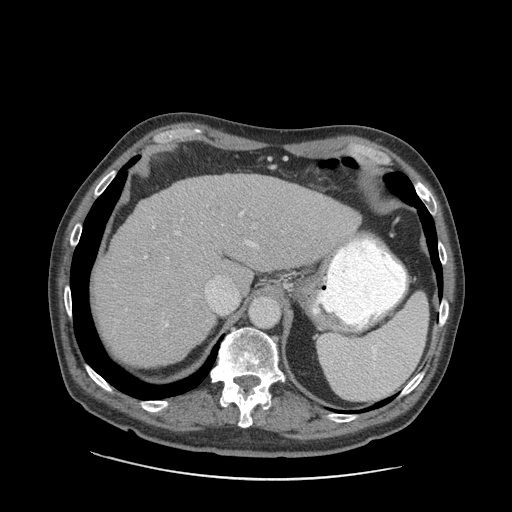
Contrast-enhanced abdominal CT (liver protocol), one axial slice. Slice 66 of 89 in the series (ordered by position). Reconstruction kernel STANDARD. 140 kVp. Soft-tissue window (W 400 / L 40 HU). 2.5 mm slice thickness. 512 × 512 image matrix. Case-level facts recorded for this patient, not image findings: diagnosis: hepatocellular carcinoma (patient treated with transarterial chemoembolisation; whether this scan precedes or follows treatment is not stated here); TNM stage (as recorded): Stage-I; Child-Pugh class: A; tumour nodularity: uninodular; tumour size: 4.6 cm.
Outlined on this slice (semi-automatically segmented with operator editing):
- liver parenchyma outside the tumour (the mass and vessels are separate outlines, so this box may not span the whole liver): box from (x=96, y=174) to (x=359, y=366) px
- liver vessels: (x=114, y=192)–(x=283, y=326)